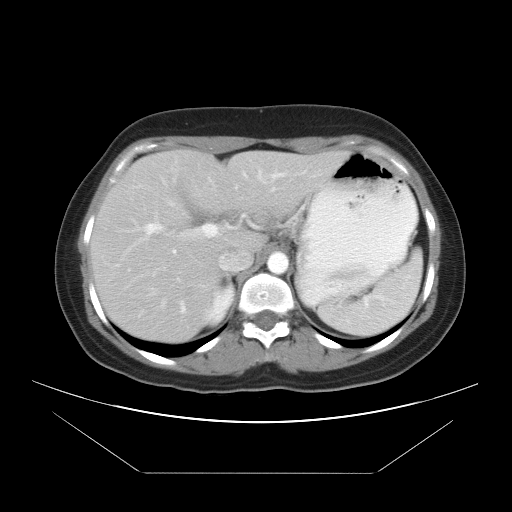
Contrast-enhanced abdominal CT, one axial slice. Position 26 of 34 along the scan axis. Soft-tissue window (W 400 / L 40 HU). 7.5 mm slice thickness. 512 × 512 image matrix, field of view 410 × 410 mm. Female patient, age 38 years. From the clinical record (not read from this slice): diagnosis: colorectal cancer liver metastases, imaged before liver resection; multiple liver metastases: yes.
Outlined on this slice (outlined manually by an expert reader):
- hepatic veins: bounding box (x1, y1, x2, y2) in pixels: (170, 189, 274, 206)
- liver: (90, 150, 348, 344)
- planned liver remnant (the part of the liver to remain after resection): (201, 151, 348, 255)
- portal vein (with intrahepatic branches): (137, 174, 283, 281)
- liver metastasis: (186, 288, 198, 299)